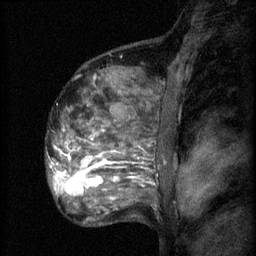
Breast MRI (dynamic contrast-enhanced), one sagittal slice; slice 44 of 60 in the series (ordered by position); 3 images stored at this slice position (order not interpretable as contrast timing); 1.5 T; TE 4.2 ms, TR 8.2 ms; 256 × 256 image matrix, field of view 180 × 180 mm. Patient: female, 48 years.
Structures marked on this image (semi-automatic segmentation, software-assisted and operator-edited):
- analysis volume of interest (the breast-tissue region the enhancement analysis was run in; not a lesion): bounding box [x1, y1, x2, y2] px = [61, 138, 153, 201]
- tumour enhancement mask (voxels above the 70 % enhancement threshold inside the analysis volume of interest): [61, 158, 120, 201]